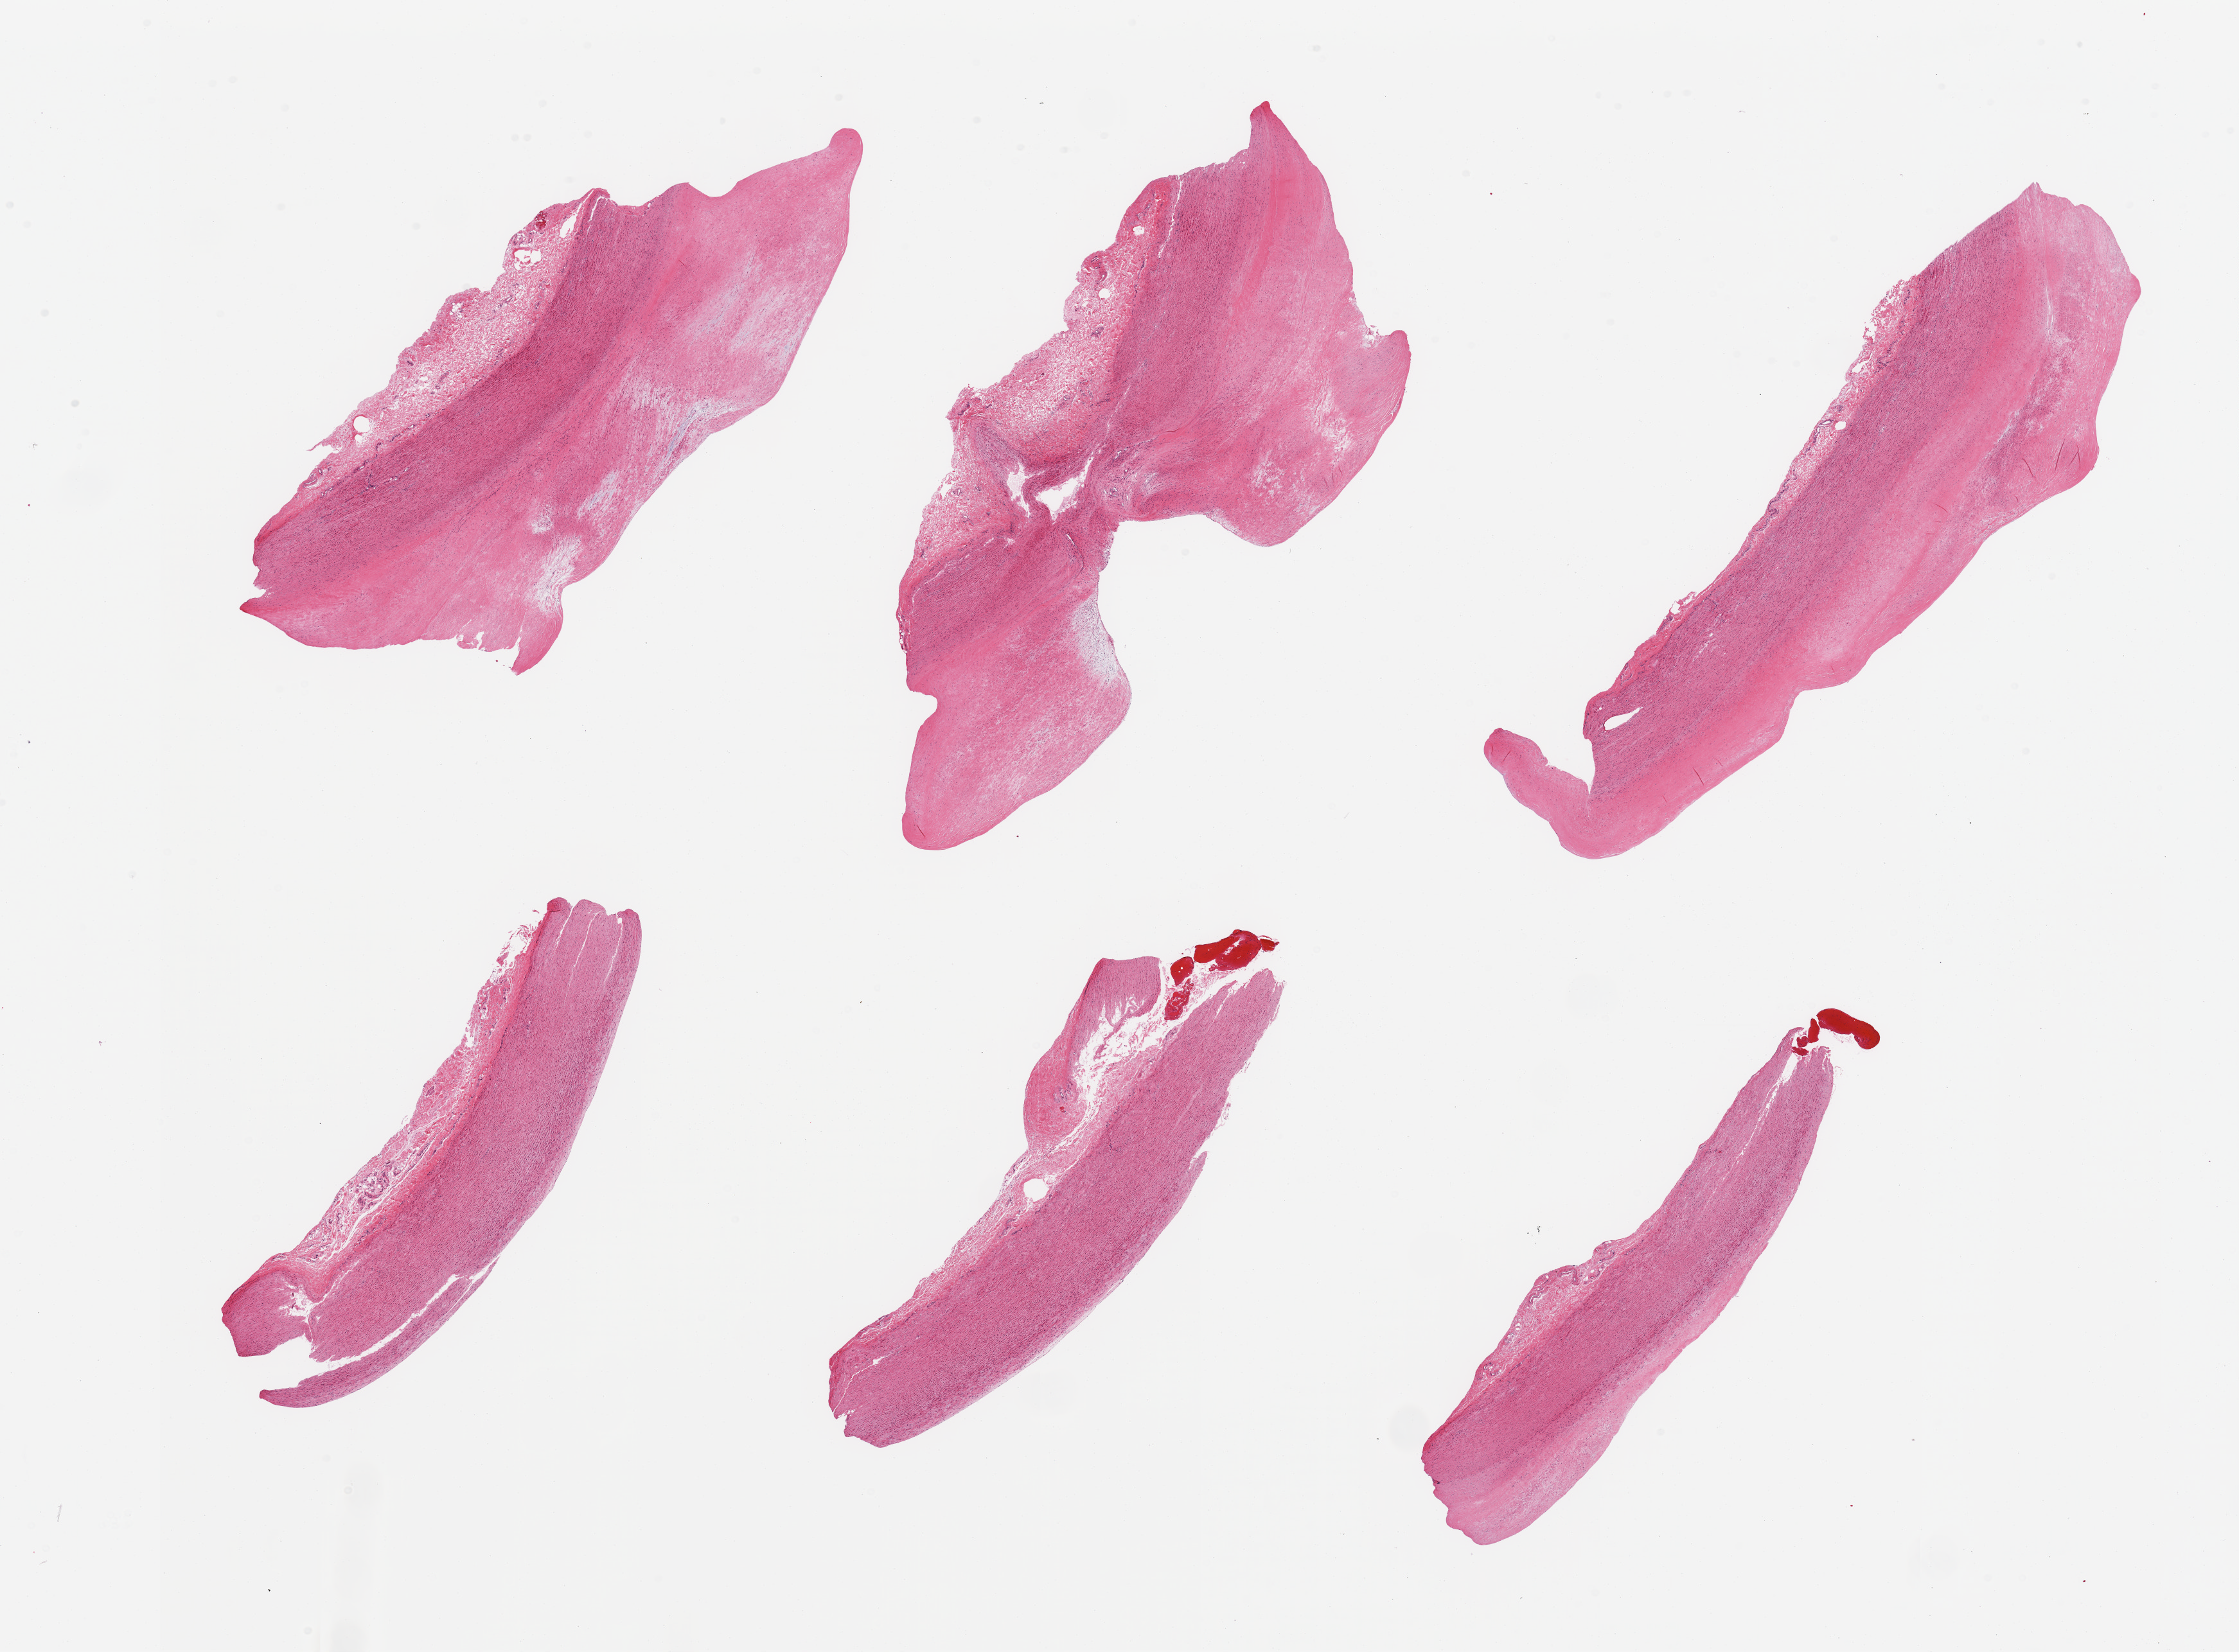
Digitized haematoxylin and eosin-stained section — shown as a low-resolution overview of the whole scanned area (about 27.6 x 20.3 mm, from a 20x scan). PAXgene-fixed paraffin-embedded (PFPE) section. Sampled site (target tissue): aorta. Donor tissue sample.
Reviewer comment on this tissue sample: 6 pieces, atherosis up to ~2mm.